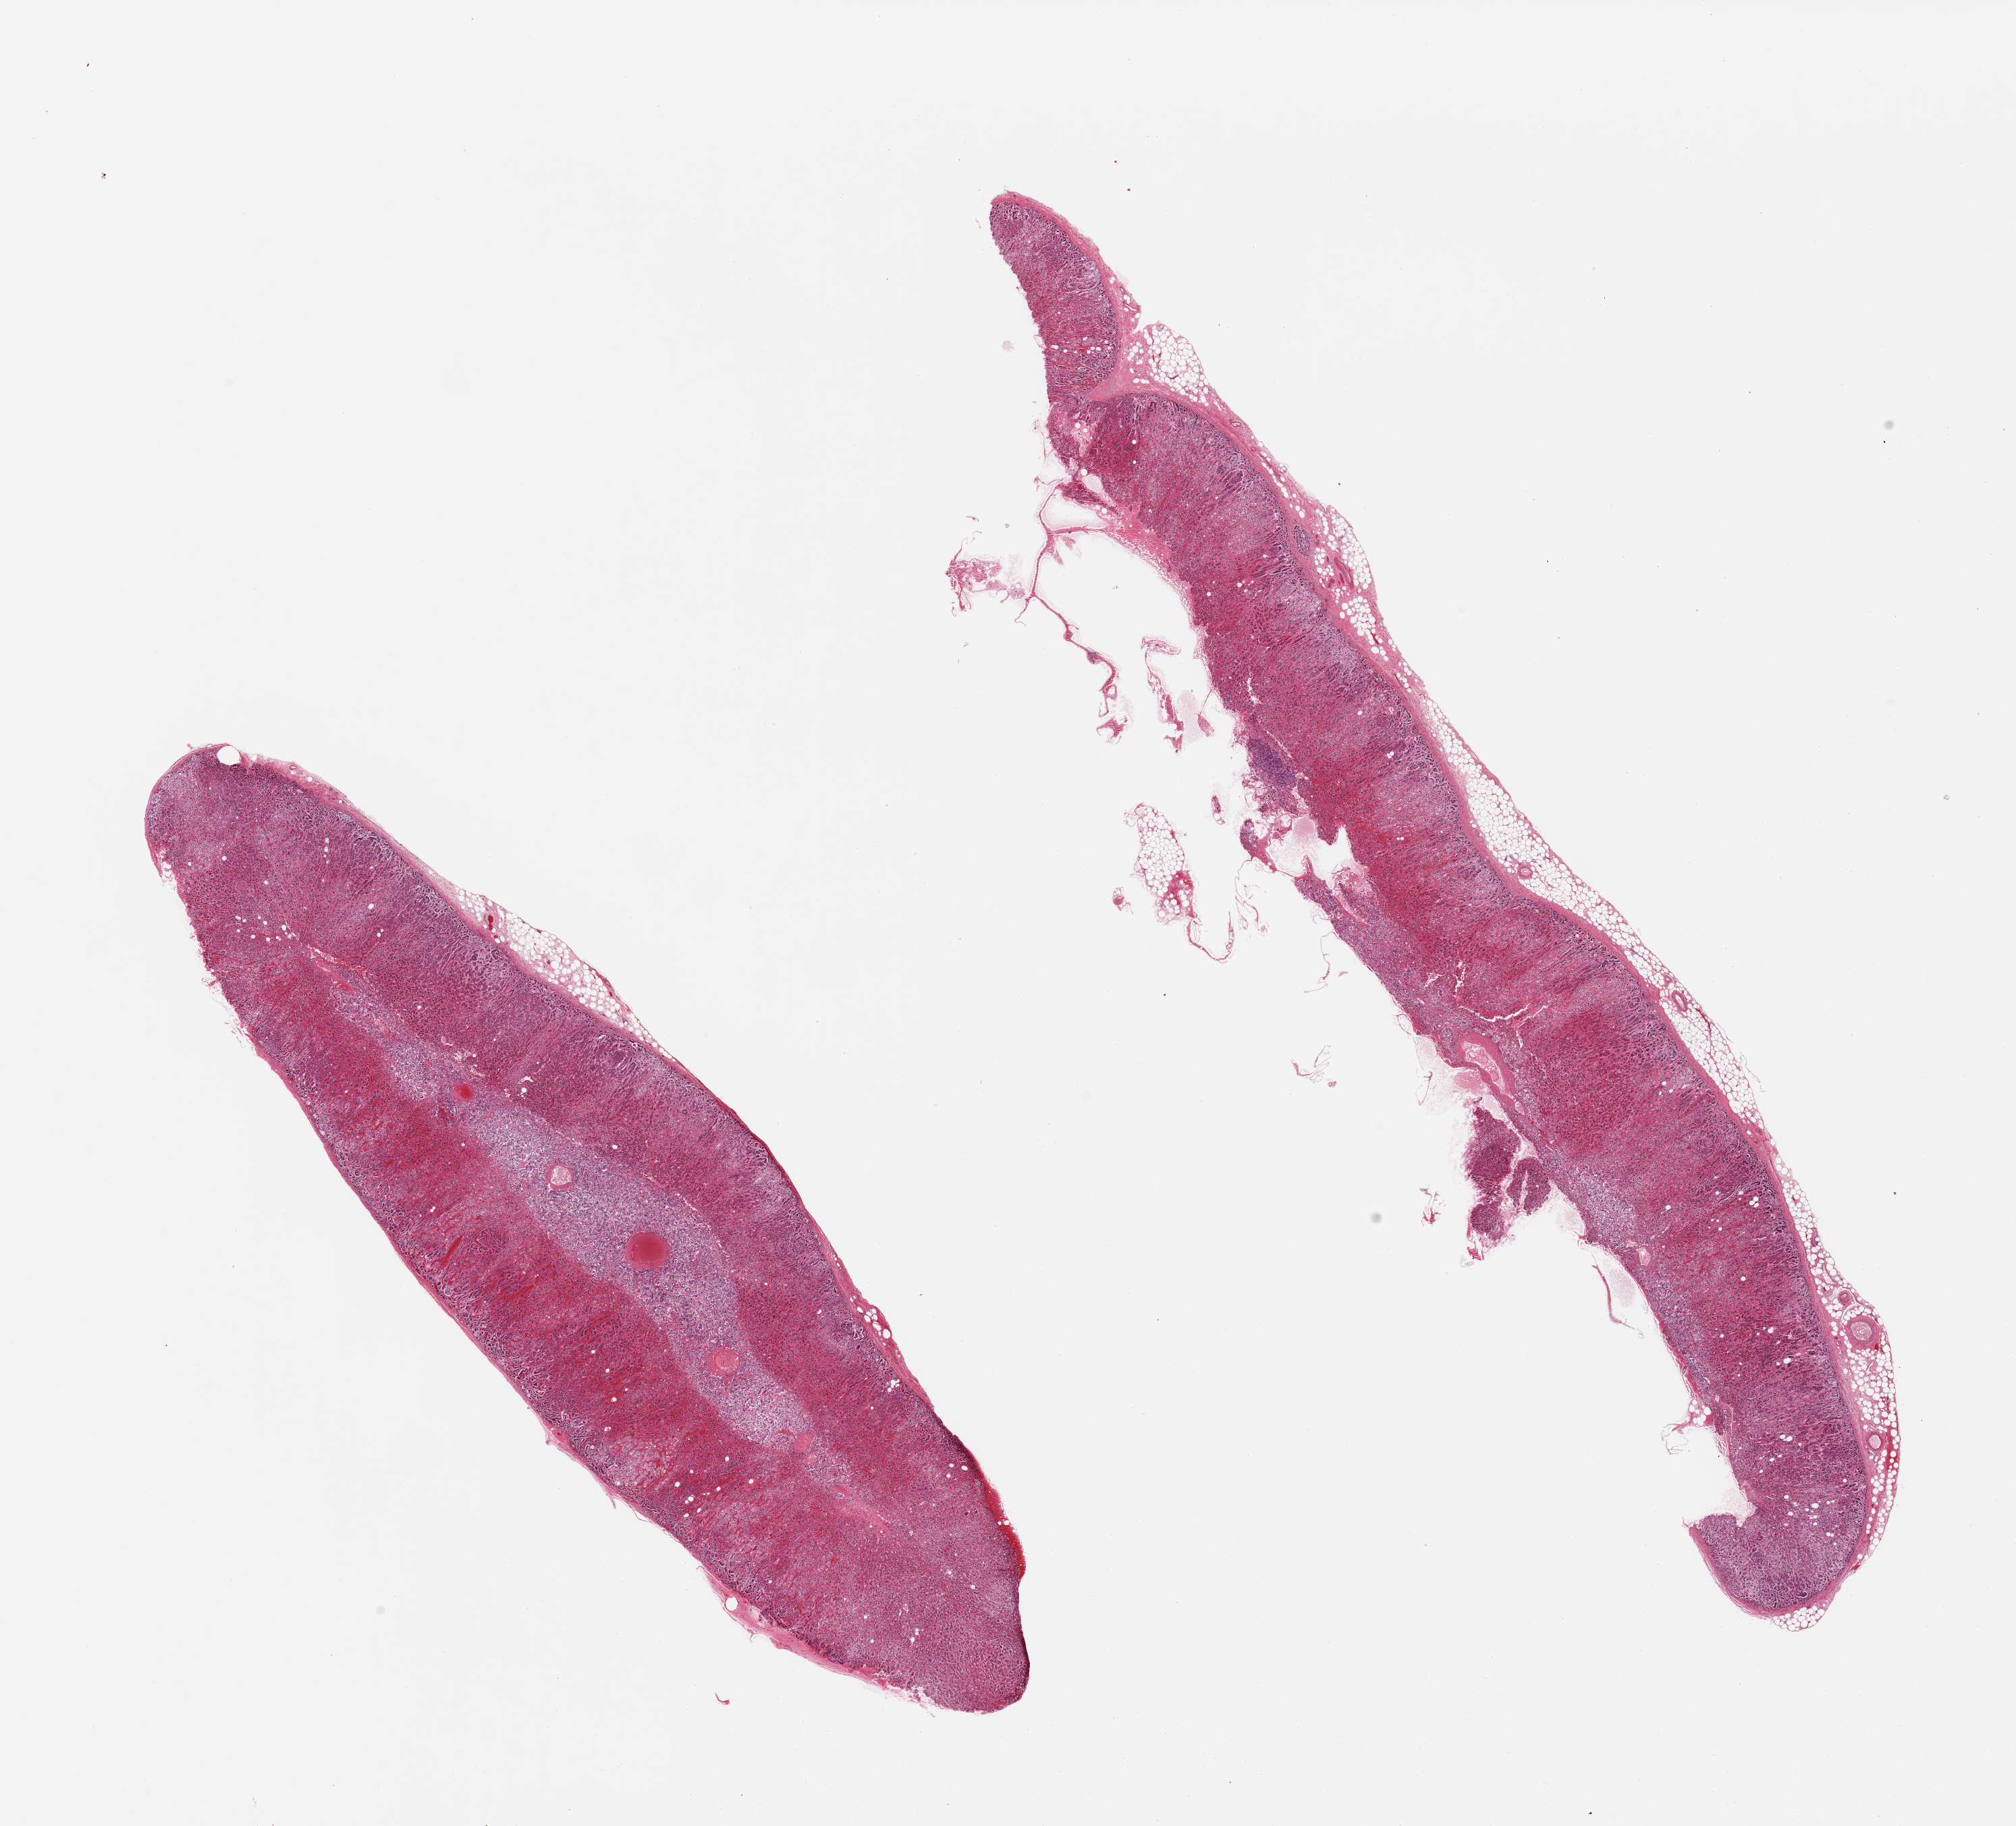
Digitized H&E-stained section, low-resolution overview of the scanned area, about 23.6 x 21.4 mm (acquisition: 20x scan), PAXgene-fixed, paraffin-embedded tissue, sampled site (target tissue): adrenal gland, tissue donor sample. Male donor.
Pathologist's review note for this sample: 2 pieces; cortex and medulla, small strip of attached adipose tissue (~10% of one piece), mild to moderate autolysis.